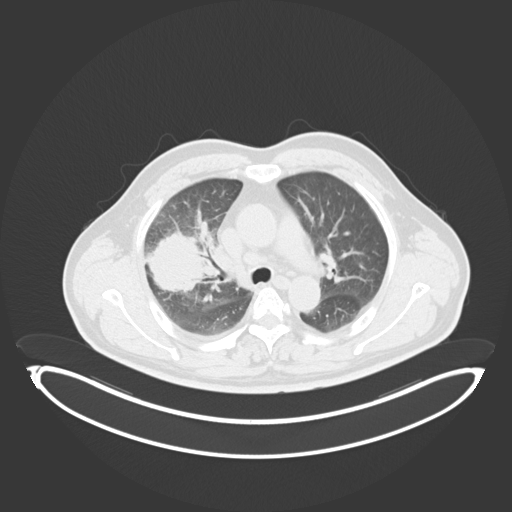
Chest CT, one axial slice; slice 218 of 284 in the series (ordered by position); reconstruction kernel B30f; lung window (W 1500 / L -600 HU); 512 × 512 image matrix. Patient: male, 55 years. Case-level facts recorded for this patient, not image findings: clinical TNM (as recorded): T3 N2 M1.
Outlined on this slice (bounding box drawn by a radiologist):
- lung tumour (recorded histology: adenocarcinoma): bounding box (x1, y1, x2, y2) in pixels: (150, 230, 209, 297)